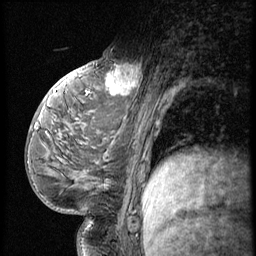
Breast MRI (dynamic contrast-enhanced), one sagittal slice; slice 31 of 56 in the series (ordered by position); 3 images stored at this slice position (order not interpretable as contrast timing); 1.5 T; TE 4.2 ms, TR 9 ms; 2.5 mm slice thickness; 256 × 256 image matrix, field of view 180 × 180 mm. Female patient, age 54 years. Case-level facts recorded for this patient, not image findings: setting: breast cancer imaged before/during neoadjuvant chemotherapy; receptor status: triple-negative.
Structures marked on this image (semi-automatic segmentation, software-assisted and operator-edited):
- analysis volume of interest (the breast-tissue region the enhancement analysis was run in; not a lesion): box from (x=99, y=53) to (x=149, y=102) px
- tumour enhancement mask (voxels above the 140 % enhancement threshold inside the analysis volume of interest): (x=107, y=63)–(x=142, y=95)